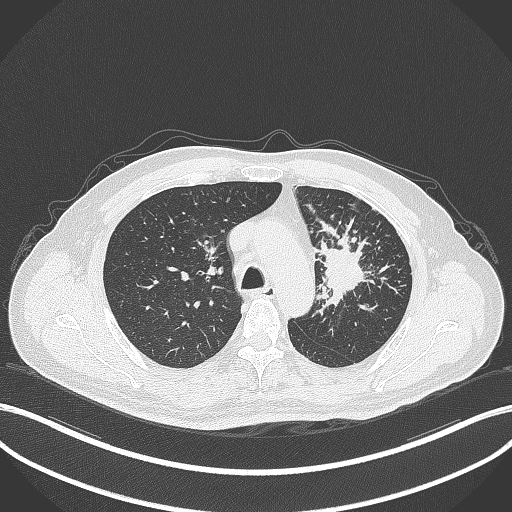
Chest CT, one axial slice; position 255 of 386 along the scan axis; reconstruction kernel B70f; 120 kVp; lung window (W 1500 / L -600 HU); 512 × 512 image matrix. Male patient, age 69 years. From the clinical record (not read from this slice): clinical TNM (as recorded): T2a N2 M0; histopathological grade: G2-3.
Structures marked on this image (rectangle marked by the reading radiologist):
- lung tumour (recorded histology: adenocarcinoma): bounding box [x1, y1, x2, y2] px = [315, 236, 367, 304]